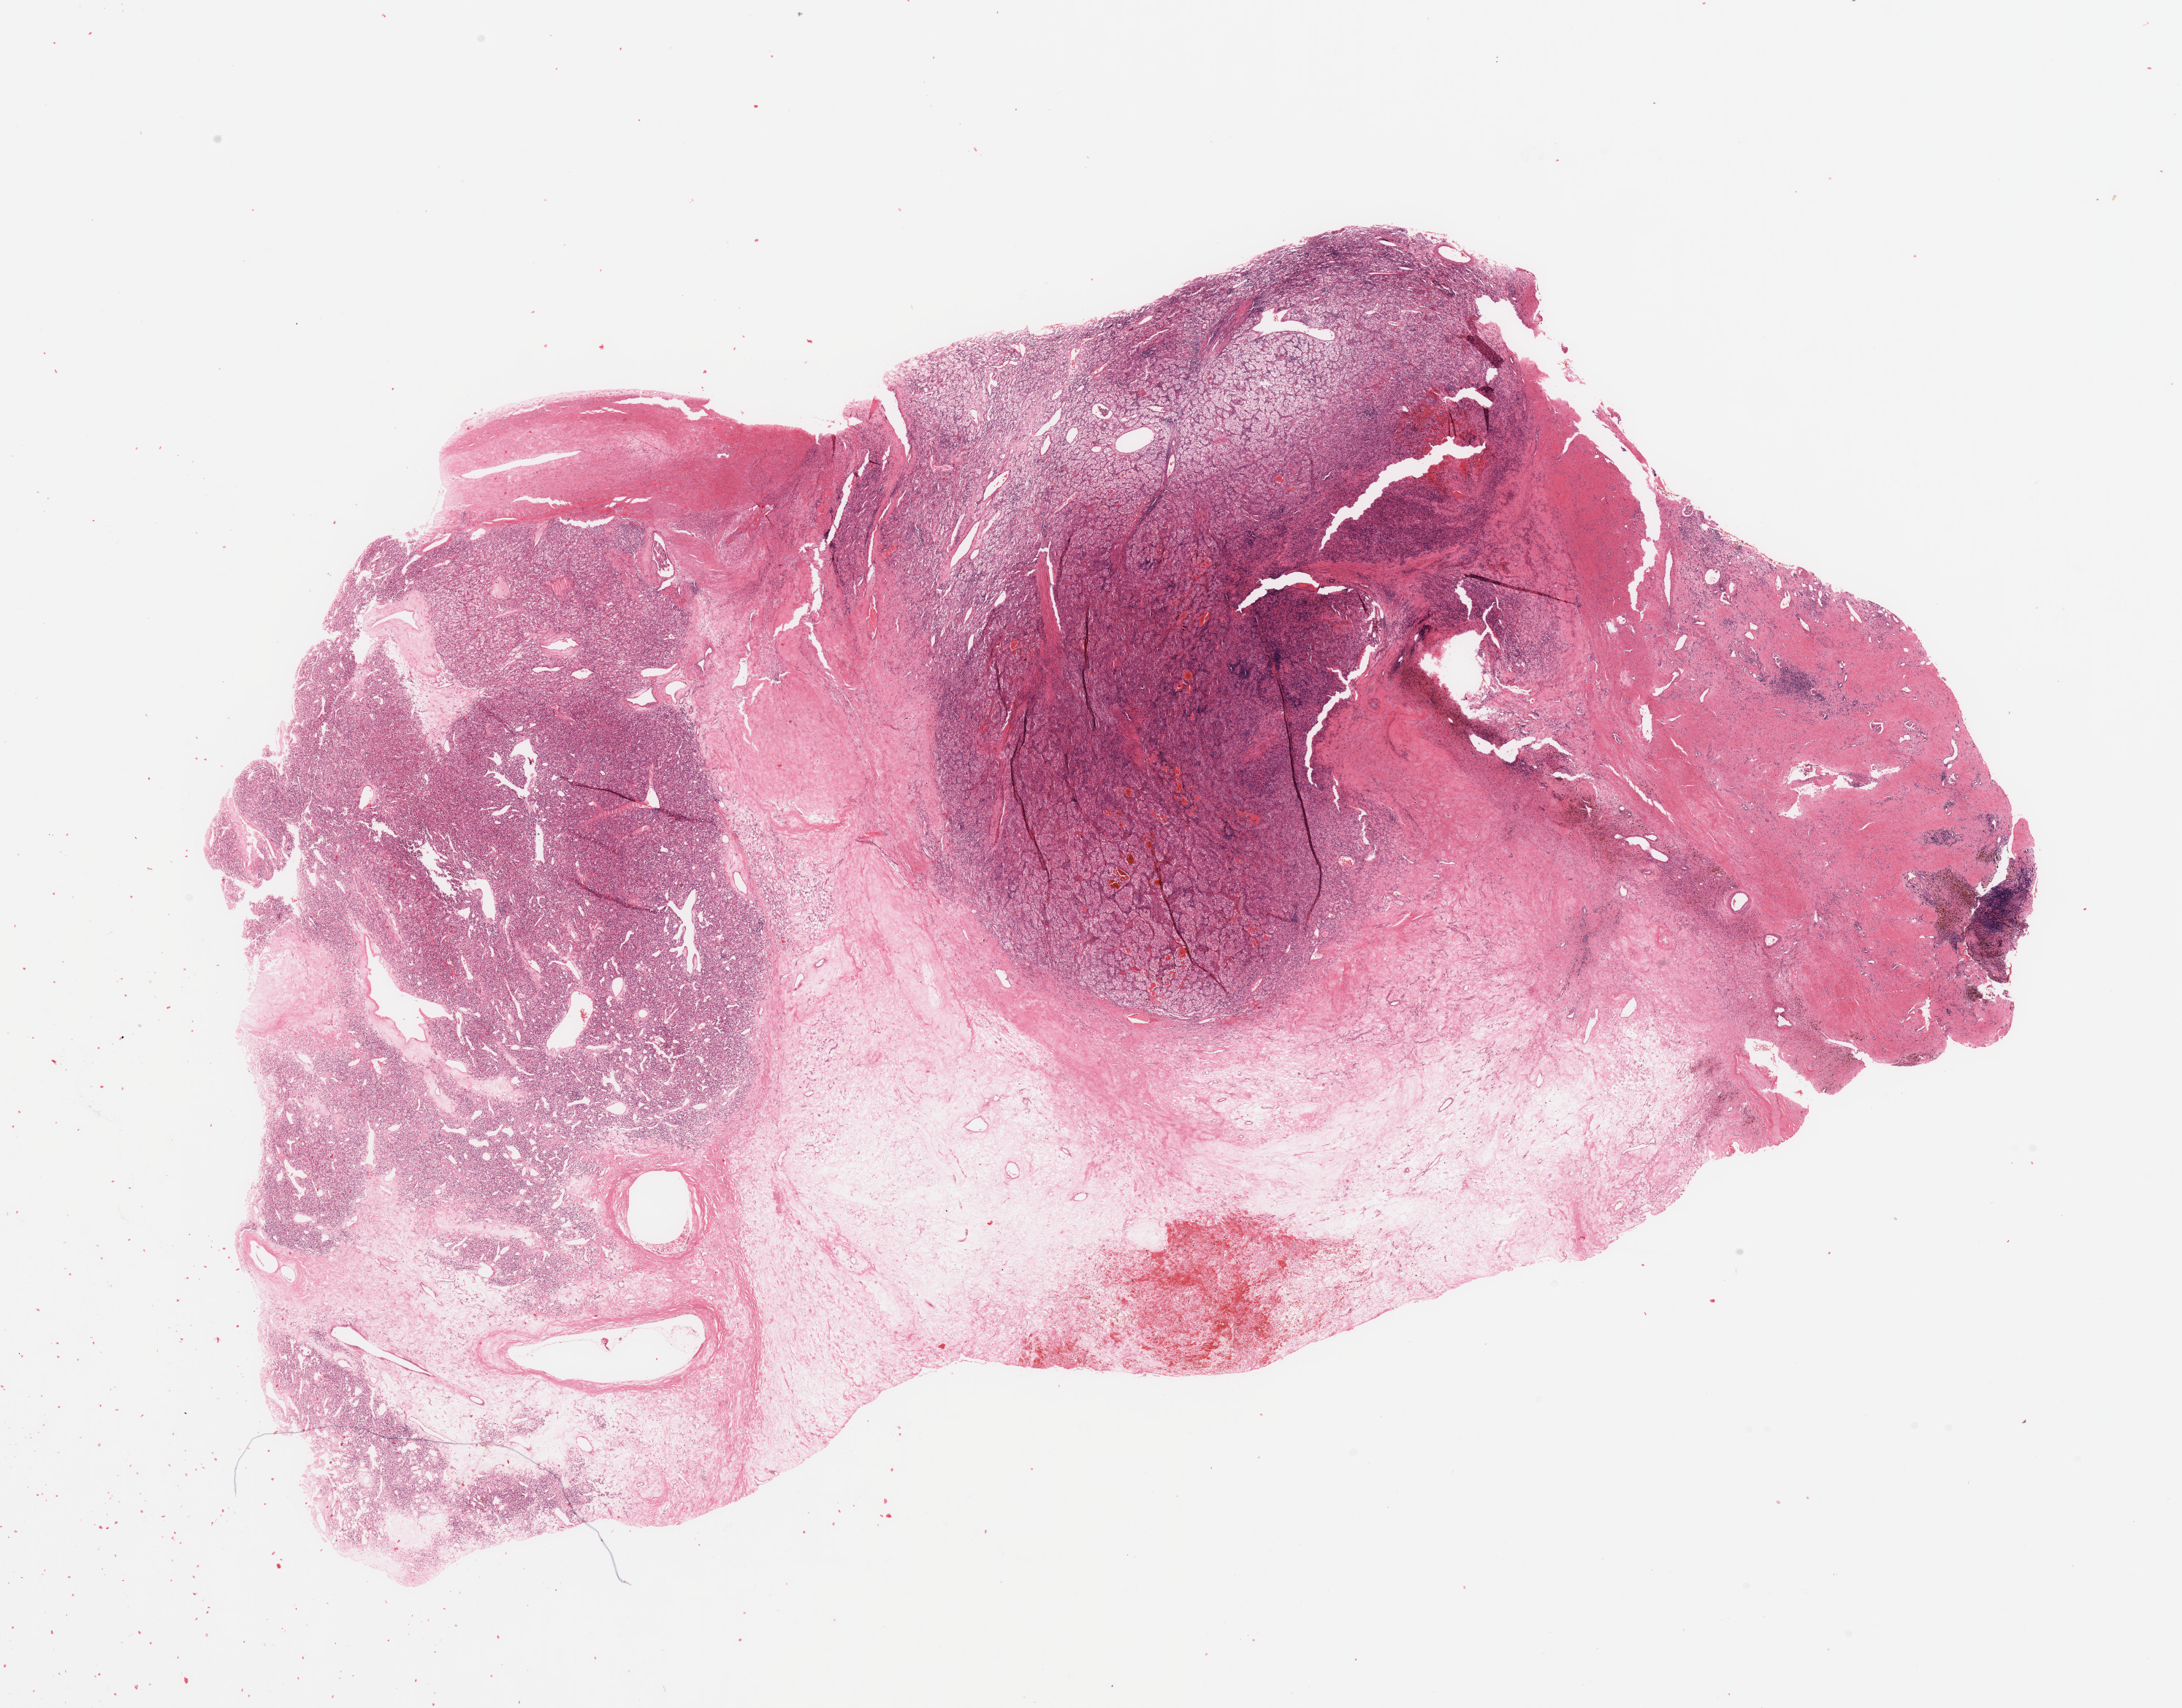
Hematoxylin and eosin (H&E) stained whole-slide image — whole scanned area (about 23.6 x 18.5 mm, from a 20x scan) shown as a low-resolution overview; tumour tissue sample, sampled site: kidney. 57-year-old female patient. Histologic grade: G2 (moderately differentiated). Pathologist review of this section (percent, as recorded): tumour nuclei 80%, necrosis 10%.
• diagnosis: Renal cell carcinoma, NOS
• AJCC pathologic stage: I